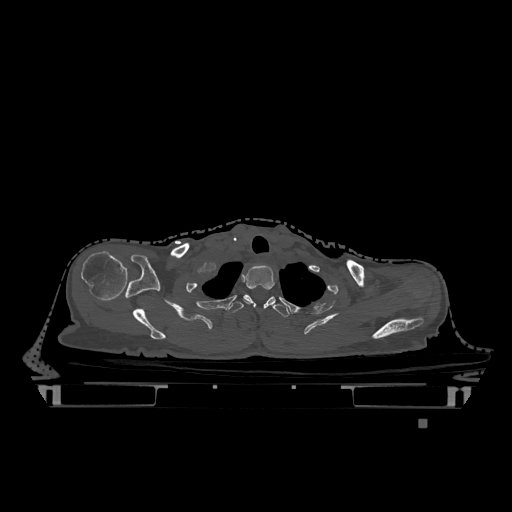
CT including the spine, one axial slice; slice 982 of 1317 in the series (ordered by position); bone window (W 1800 / L 400 HU); 512 × 512 image matrix, field of view 500 × 500 mm. Female patient, age 74 years. Case-level facts recorded for this patient, not image findings: primary cancer: lung.
Outlined on this slice (semi-automatic segmentation, software-assisted and operator-edited):
- T1 vertebra: bounding box [x1, y1, x2, y2] px = [244, 265, 275, 304]
- T2 vertebra: [227, 294, 290, 317]